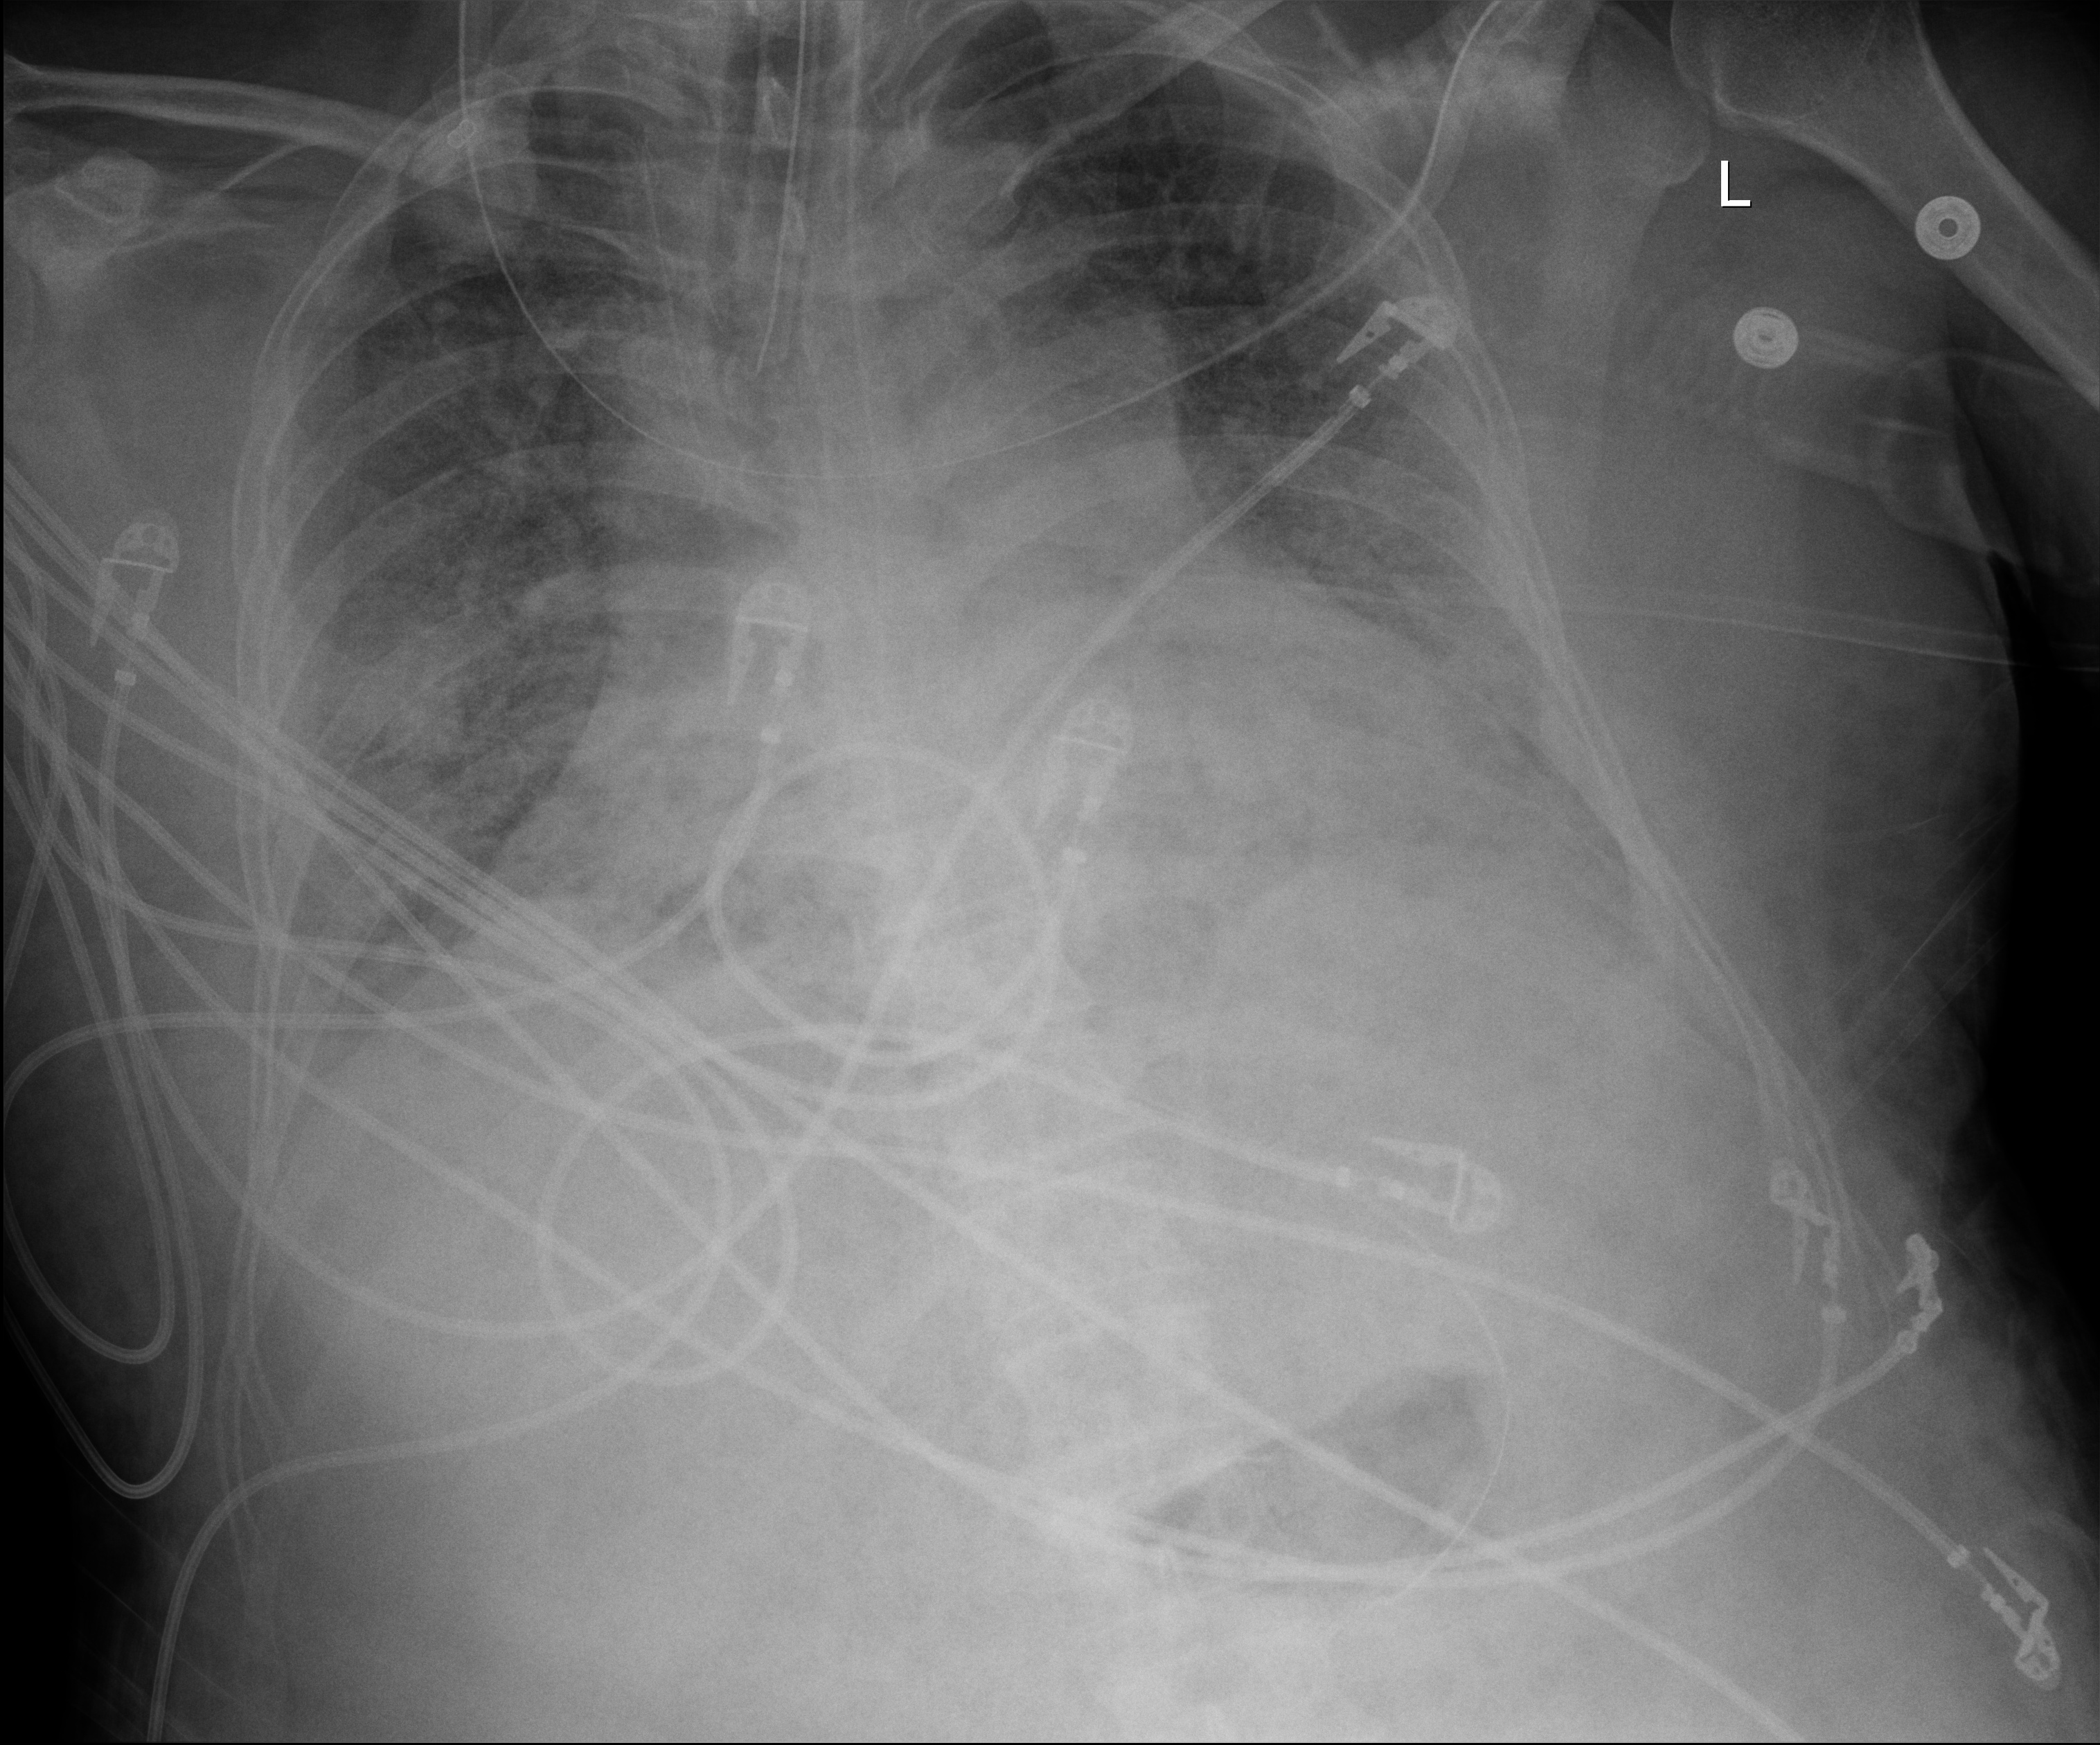
Bedside chest radiograph (digital radiography). Adult patient hospitalised with COVID-19, age 18–59 years.
Hospital-stay facts (about this admission, not read from this image; timing relative to this image not recorded): mechanically ventilated during this hospital stay: yes.